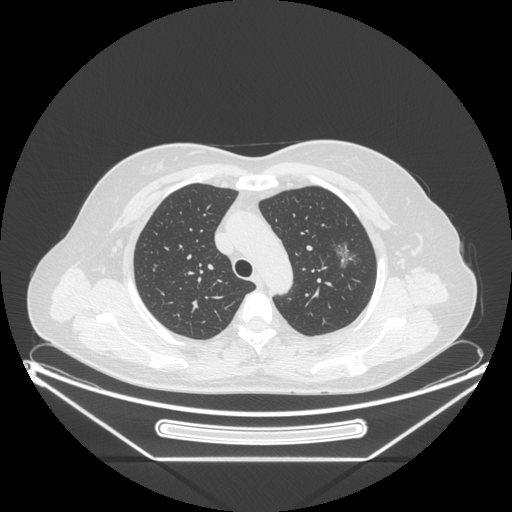
Chest CT, one axial slice; position 163 of 226 along the scan axis; reconstruction kernel STANDARD; 120 kVp; lung window (W 1500 / L -600 HU); 1.25 mm slice thickness; 512 × 512 image matrix, field of view 447 × 447 mm. Patient: female, 54 years. Case-level facts recorded for this patient, not image findings: clinical TNM (as recorded): T1c N0 M0.
Structures marked on this image (rectangle marked by the reading radiologist):
- lung tumour (recorded histology: adenocarcinoma): bounding box <327,237,361,279> (left, top, right, bottom; pixels)